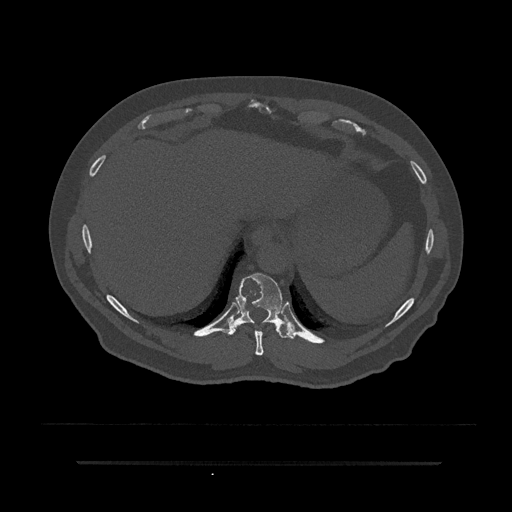
CT including the spine, one axial slice; slice 345 of 797 in the series (ordered by position); reconstruction kernel Br40s/3; 120 kVp; bone window (W 1800 / L 400 HU); 0.5 mm slice thickness; 512 × 512 image matrix, field of view 464 × 464 mm. Patient: male, 59 years. Case-level facts recorded for this patient, not image findings: primary cancer: bile ducts.
Annotated regions visible in this slice (semi-automatically segmented with operator editing):
- T10 vertebra: bounding box <227,273,294,339> (left, top, right, bottom; pixels)
- T9 vertebra: <254,330,264,356>